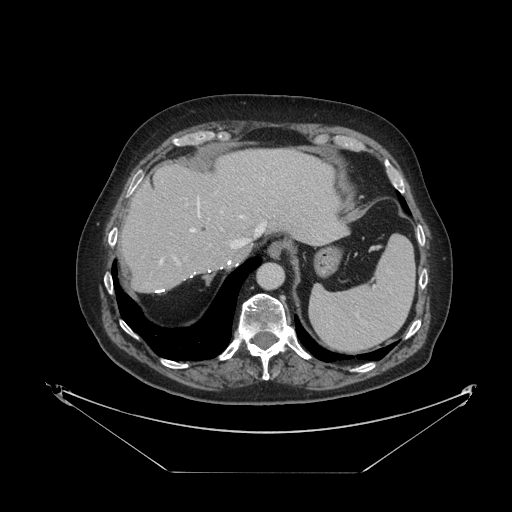
Contrast-enhanced abdominal CT, one axial slice. Slice 90 of 121 in the series (ordered by position). Reconstruction kernel STANDARD. Intravenous contrast given. Soft-tissue window (W 400 / L 40 HU). 2.5 mm slice thickness. 512 × 512 image matrix. Male patient, age 68 years. Case-level facts recorded for this patient, not image findings: diagnosis: colorectal cancer liver metastases, imaged before liver resection.
Outlined on this slice (outlined manually by an expert reader):
- hepatic veins: bounding box (x1, y1, x2, y2) in pixels: (160, 197, 266, 263)
- liver: (121, 149, 345, 293)
- planned liver remnant (the part of the liver to remain after resection): (121, 149, 345, 292)
- portal vein (with intrahepatic branches): (175, 210, 223, 265)